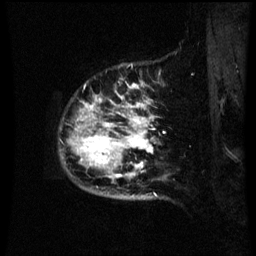
Breast MRI (dynamic contrast-enhanced), one sagittal slice; slice 58 of 60 in the series (ordered by position); dynamic contrast-enhanced series, image 2 of 3 at this slice position (ordered by acquisition); 1.5 T; TE 4.2 ms, TR 8.9 ms; 256 × 256 image matrix, field of view 200 × 200 mm. Female patient, age 42 years. Case-level facts recorded for this patient, not image findings: setting: breast cancer imaged before/during neoadjuvant chemotherapy; receptor status: HER2-positive.
Outlined on this slice (semi-automatically segmented with operator editing):
- analysis volume of interest (the breast-tissue region the enhancement analysis was run in; not a lesion): box from (x=66, y=82) to (x=171, y=193) px
- tumour enhancement mask (voxels above the 70 % enhancement threshold inside the analysis volume of interest): (x=70, y=86)–(x=153, y=179)